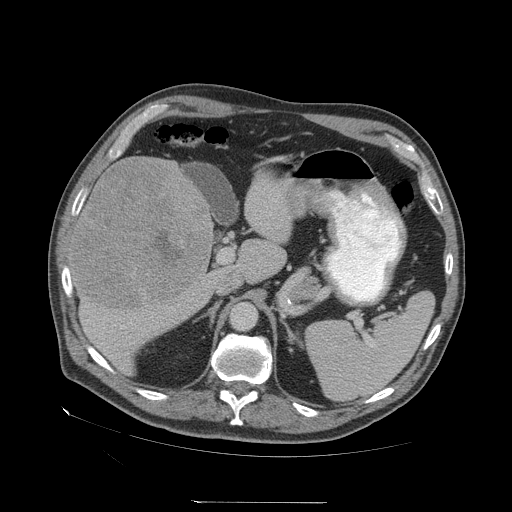
Contrast-enhanced abdominal CT (liver protocol), one axial slice; position 32 of 83 along the scan axis; reconstruction kernel STANDARD; 140 kVp; soft-tissue window (W 400 / L 40 HU); 2.5 mm slice thickness; 512 × 512 image matrix, field of view 460 × 460 mm. From the clinical record (not read from this slice): diagnosis: hepatocellular carcinoma (patient treated with transarterial chemoembolisation; whether this scan precedes or follows treatment is not stated here); TNM stage (as recorded): Stage-I; Child-Pugh class: A; tumour differentiation: well differentiated.
Annotated regions visible in this slice (semi-automatically segmented with operator editing):
- liver parenchyma outside the tumour (the mass and vessels are separate outlines, so this box may not span the whole liver): bounding box [x1, y1, x2, y2] px = [68, 156, 212, 374]
- mass: [71, 156, 211, 309]